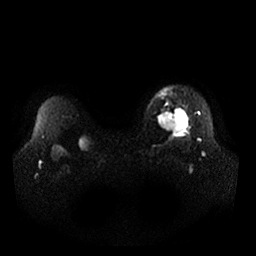
Breast MRI, one axial slice; diffusion-weighted series; image 2 of 4 stored at this slice position (different b-values; order by instance number); 1.5 T; 4 mm slice thickness; 256 × 256 image matrix. Female patient.
Structures marked on this image (outlined manually by an expert reader):
- tumour on diffusion-weighted imaging: bounding box (x1, y1, x2, y2) in pixels: (158, 110, 189, 132)